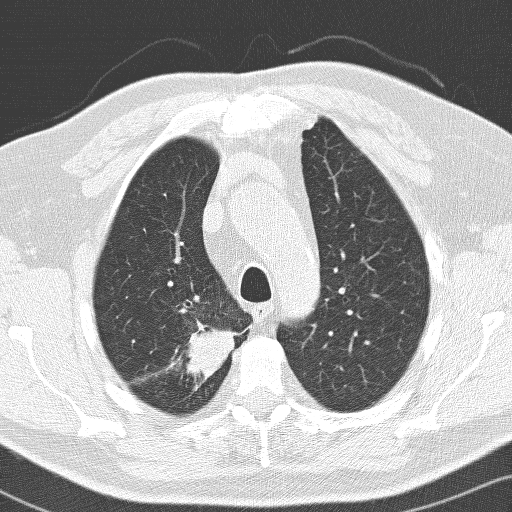
Axial slice from a low-dose chest CT screening exam, baseline annual screen, lung window (W 1500 / L -600 HU), 3.2 mm slice thickness, lung (sharp) reconstruction kernel (D), 120 kVp, slice 30 of 141 in the series. Male participant, aged 66 years at enrolment. Former smoker at enrolment.
Lesion marked by an expert reader, bounding box (x1, y1, x2, y2) in pixels: (152, 310, 231, 392). Screening reader's record for this exam (one nodule recorded; not confirmed to be the boxed lesion): non-calcified nodule or mass ≥4 mm, right upper lobe, 36 × 30 mm, spiculated (stellate) margins, soft tissue attenuation. Official screen result: positive, change unspecified: nodule(s) >= 4 mm or enlarging nodule(s), mass(es), or other non-specific abnormalities suspicious for lung cancer. Lung cancer was diagnosed 103 days after this screen: adenocarcinoma, NOS, right upper lobe, poorly differentiated (G3), stage IIB (AJCC 6th edition), 33 mm at pathology.